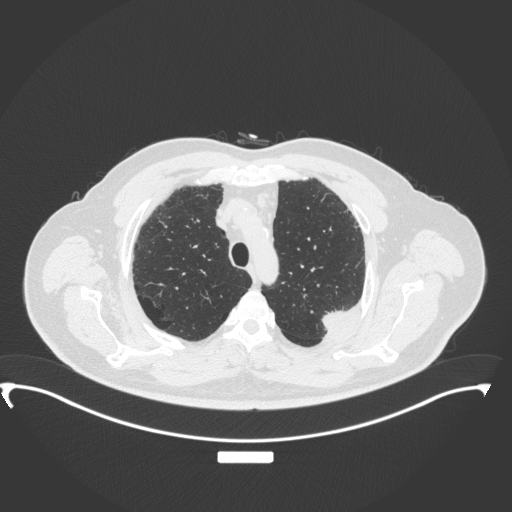
Chest CT, one axial slice. Position 286 of 350 along the scan axis. Reconstruction kernel B31f. 120 kVp. Lung window (W 1500 / L -600 HU). 1 mm slice thickness. 512 × 512 image matrix. Patient: male, 64 years. Case-level facts recorded for this patient, not image findings: clinical TNM (as recorded): T1c N1 M1.
Outlined on this slice (rectangle marked by the reading radiologist):
- lung tumour (recorded histology: adenocarcinoma): bounding box [x1, y1, x2, y2] px = [317, 304, 358, 338]